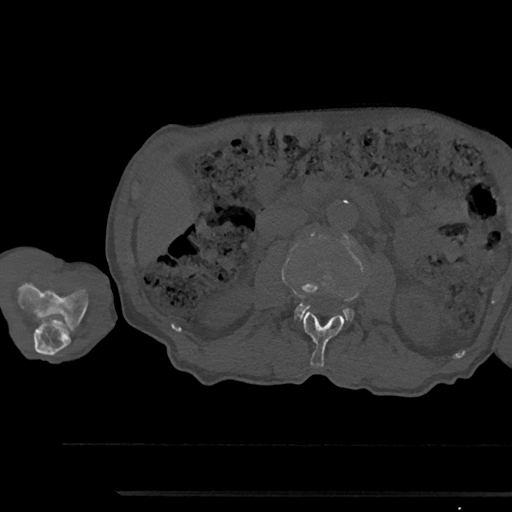
CT including the spine, one axial slice; slice 532 of 797 in the series (ordered by position); bone window (W 1800 / L 400 HU); 0.5 mm slice thickness; 512 × 512 image matrix. Patient: male, 79 years. From the clinical record (not read from this slice): primary cancer: prostate.
Structures marked on this image (semi-automatic segmentation, software-assisted and operator-edited):
- L2 vertebra: bounding box [x1, y1, x2, y2] px = [302, 312, 345, 367]
- L3 vertebra: [295, 236, 354, 320]